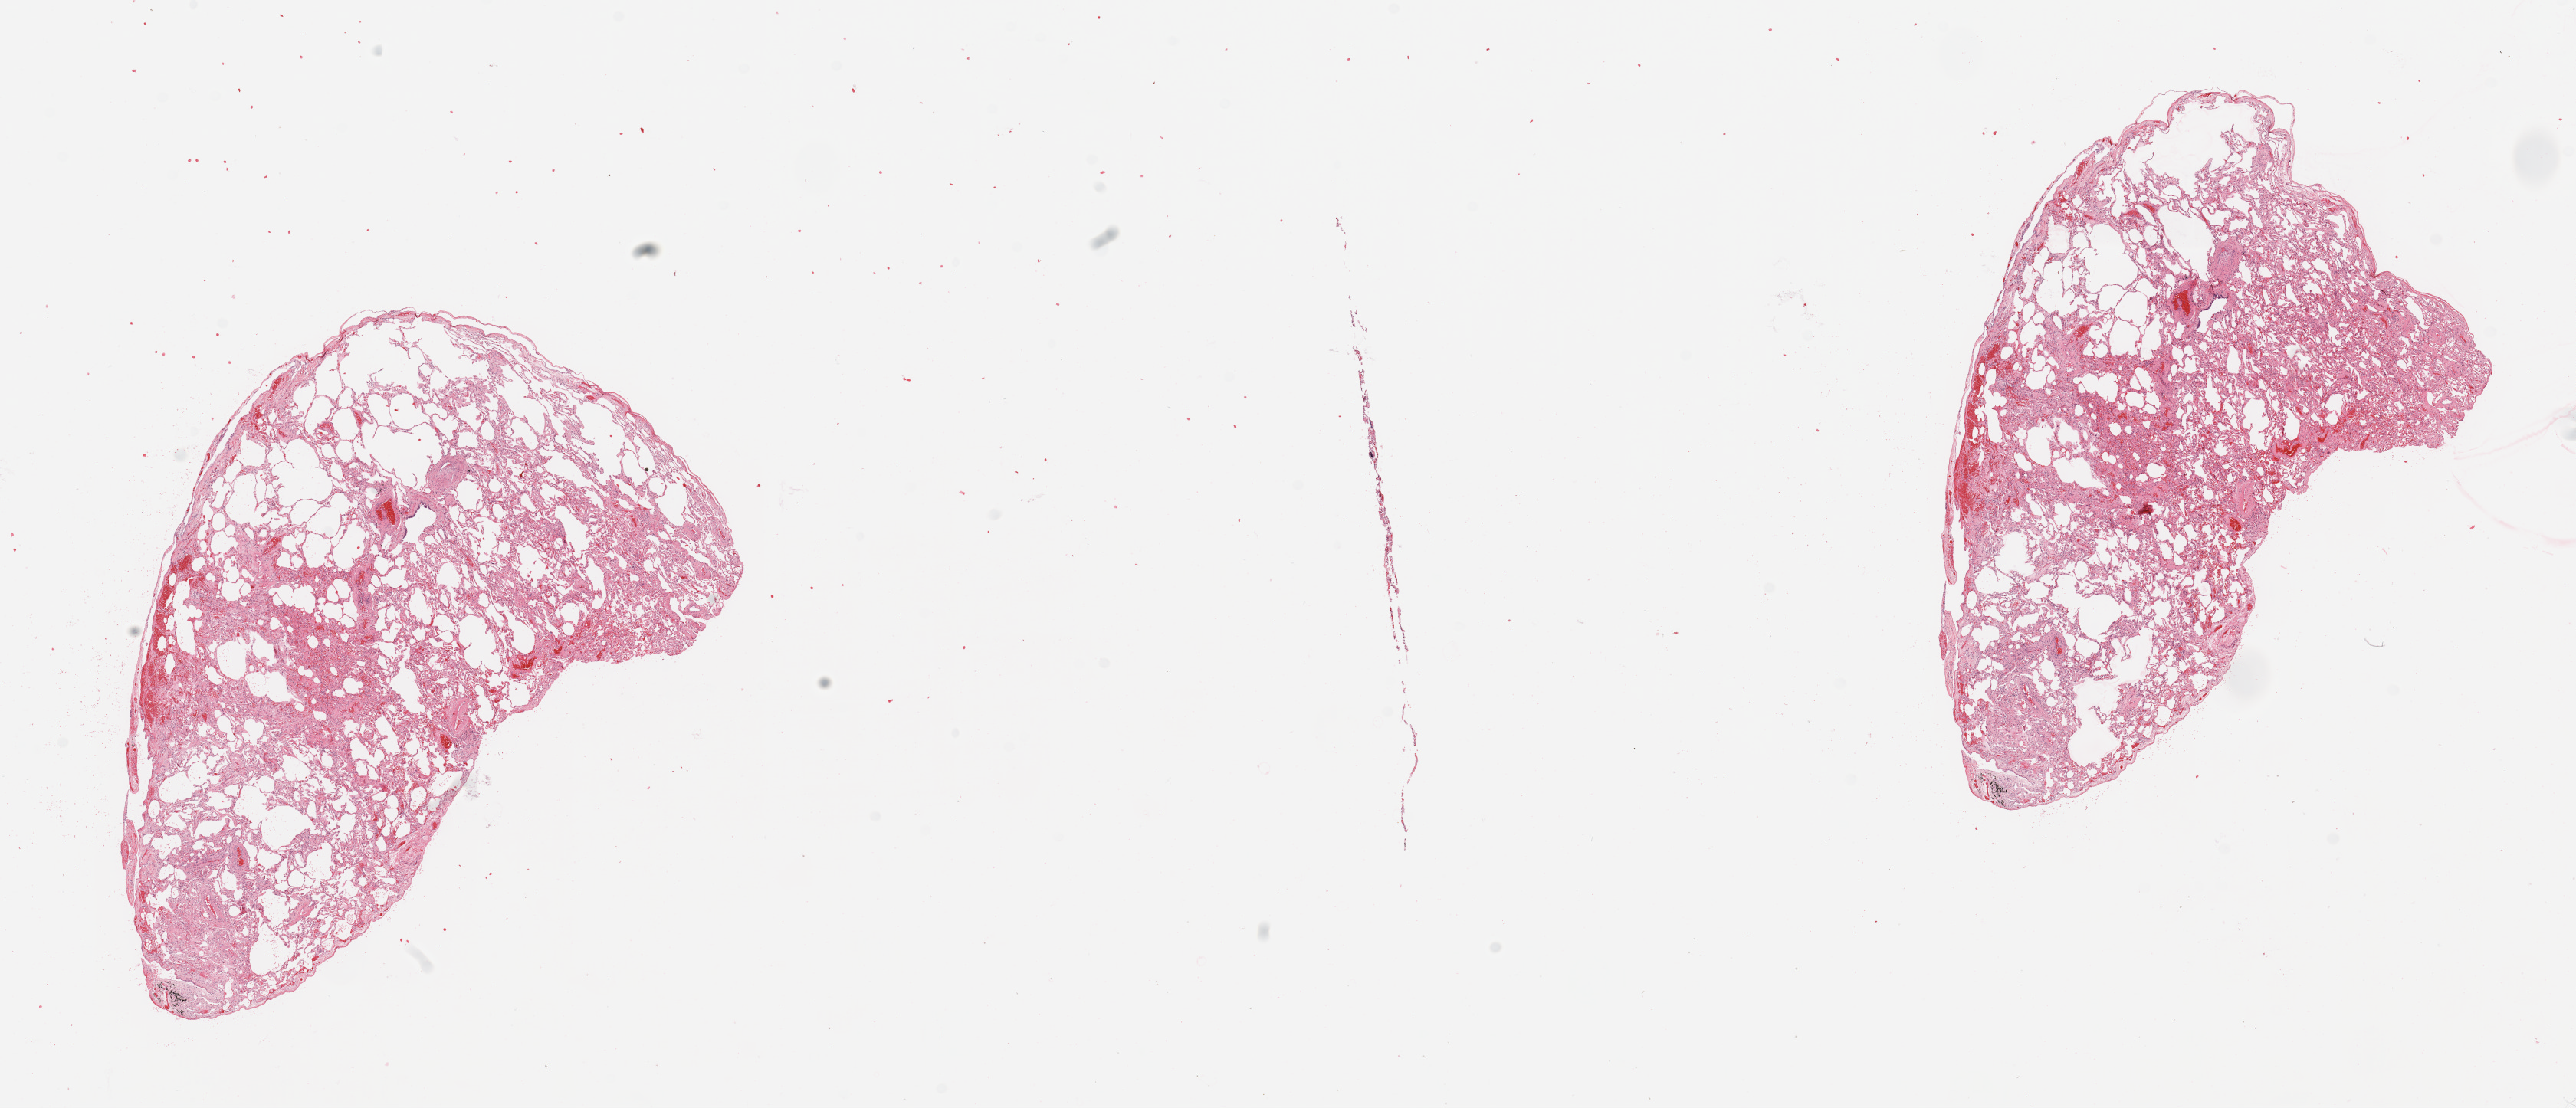
Whole-slide histology image, Hematoxylin and eosin (H&E) stained — shown as a low-resolution overview of the whole scanned area (about 26.6 x 11.4 mm, slide scanned at 20x). Normal (non-tumour) tissue sample, sampled site: lung. Male, 78 y/o.
This section: normal (non-tumour) tissue from the same patient. Patient diagnosis: Adenocarcinoma, NOS.